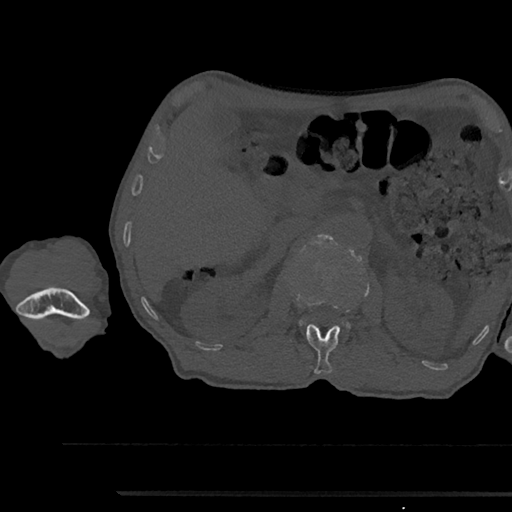
CT including the spine, one axial slice. Slice 612 of 797 in the series (ordered by position). Reconstruction kernel Br40s/3. 120 kVp. Bone window (W 1800 / L 400 HU). 0.5 mm slice thickness. 512 × 512 image matrix, field of view 367 × 367 mm. Male patient, age 79 years. Case-level facts recorded for this patient, not image findings: primary cancer: prostate.
Structures marked on this image (semi-automatically segmented with operator editing):
- L1 vertebra: bounding box [x1, y1, x2, y2] px = [296, 296, 340, 374]
- L2 vertebra: [300, 234, 350, 328]